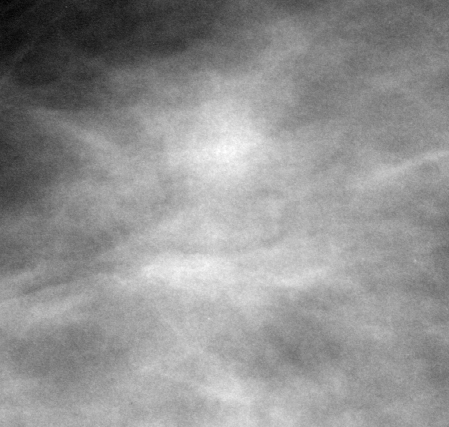
Cropped region of a digitized screen-film mammogram centred on a radiologist-marked abnormality; right breast; MLO view; BI-RADS breast density category 2 (scale 1–4).
Finding: mass, shape architectural distortion, margins spiculated; BI-RADS assessment category 4; benign without callback (not worked up further).